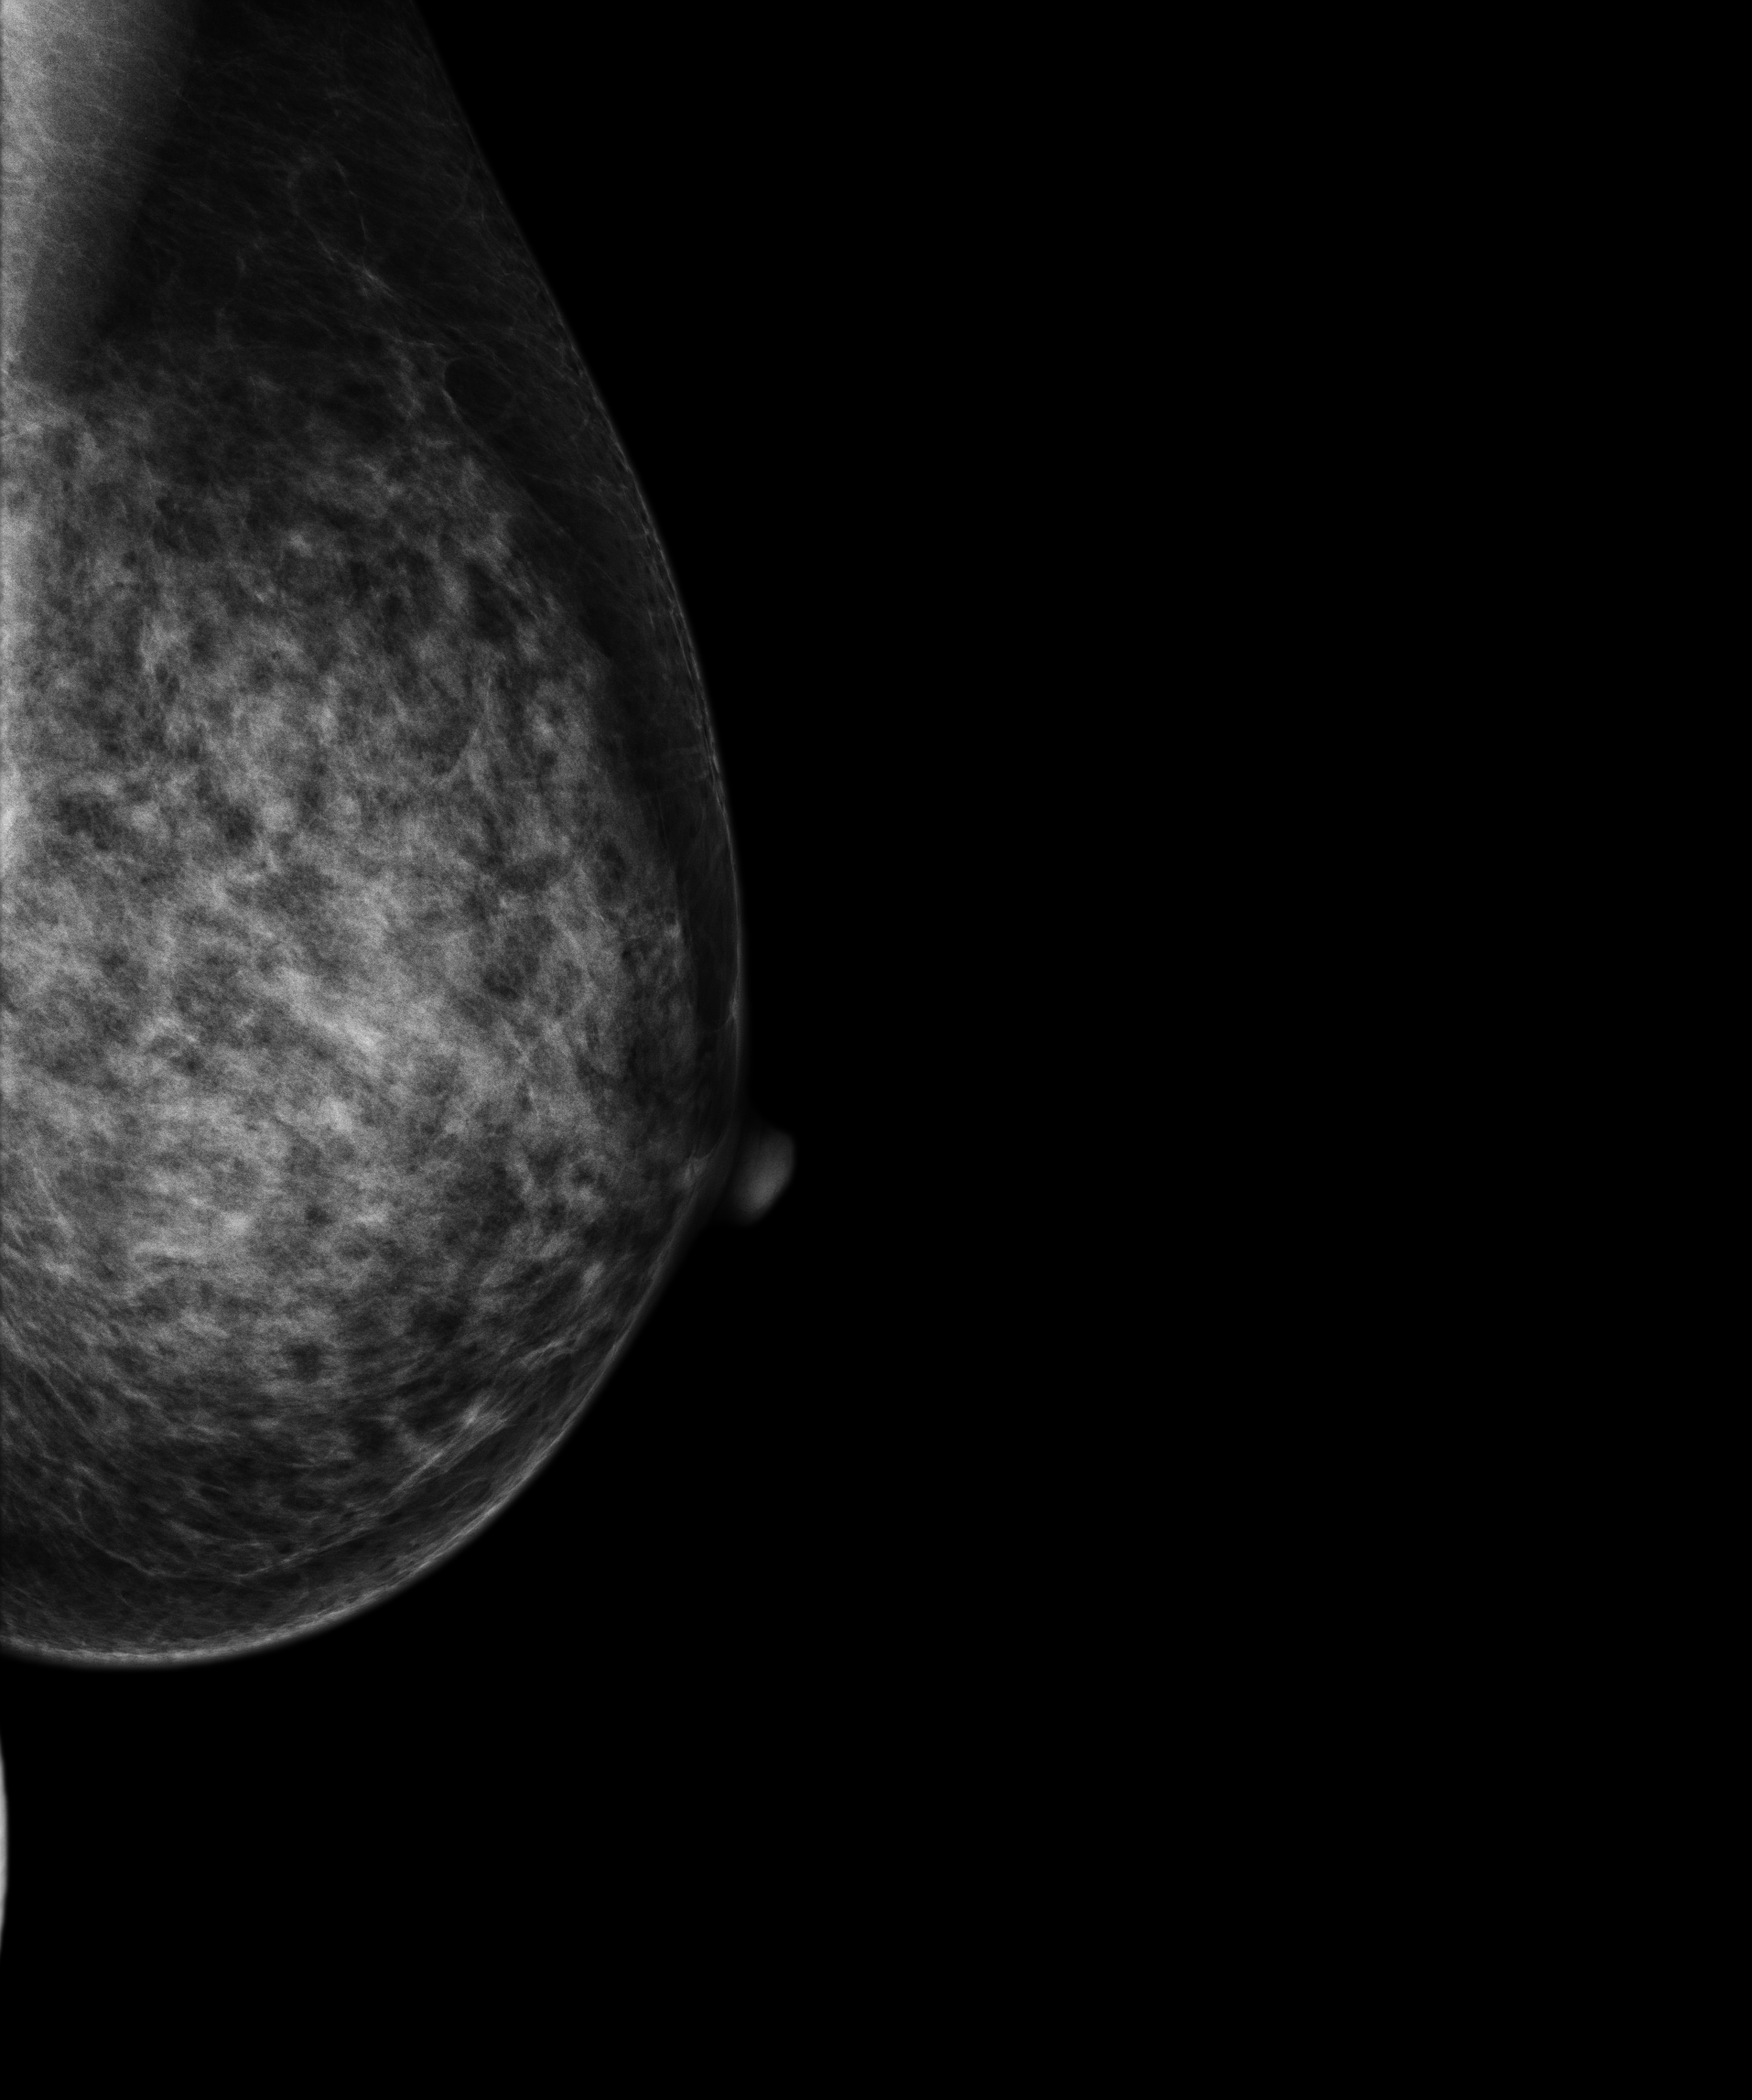
Digital mammogram (FFDM); left breast; laterally exaggerated craniocaudal (XCCL) view; screening examination; compressed breast thickness 49 mm. Patient: female, 60 years.
- breast density at the screening exam (both breasts): extremely dense (BI-RADS density category d)
- final BI-RADS assessment for this screening round (tomosynthesis exam, both breasts): category 1
- recall: no recall after this screen